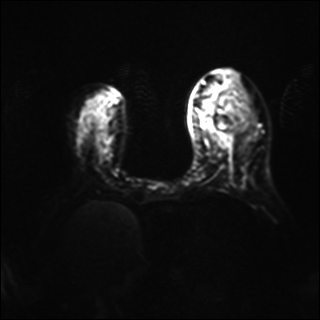
Breast MRI, one axial slice. Slice 18 of 40 in the series (ordered by position). Diffusion-weighted series; image 2 of 4 stored at this slice position (different b-values; order by instance number). 1.5 T. 4 mm slice thickness. 320 × 320 image matrix, field of view 320 × 320 mm. Female patient.
Outlined on this slice (manually delineated by an expert):
- tumour on diffusion-weighted imaging: bounding box <216,99,249,132> (left, top, right, bottom; pixels)